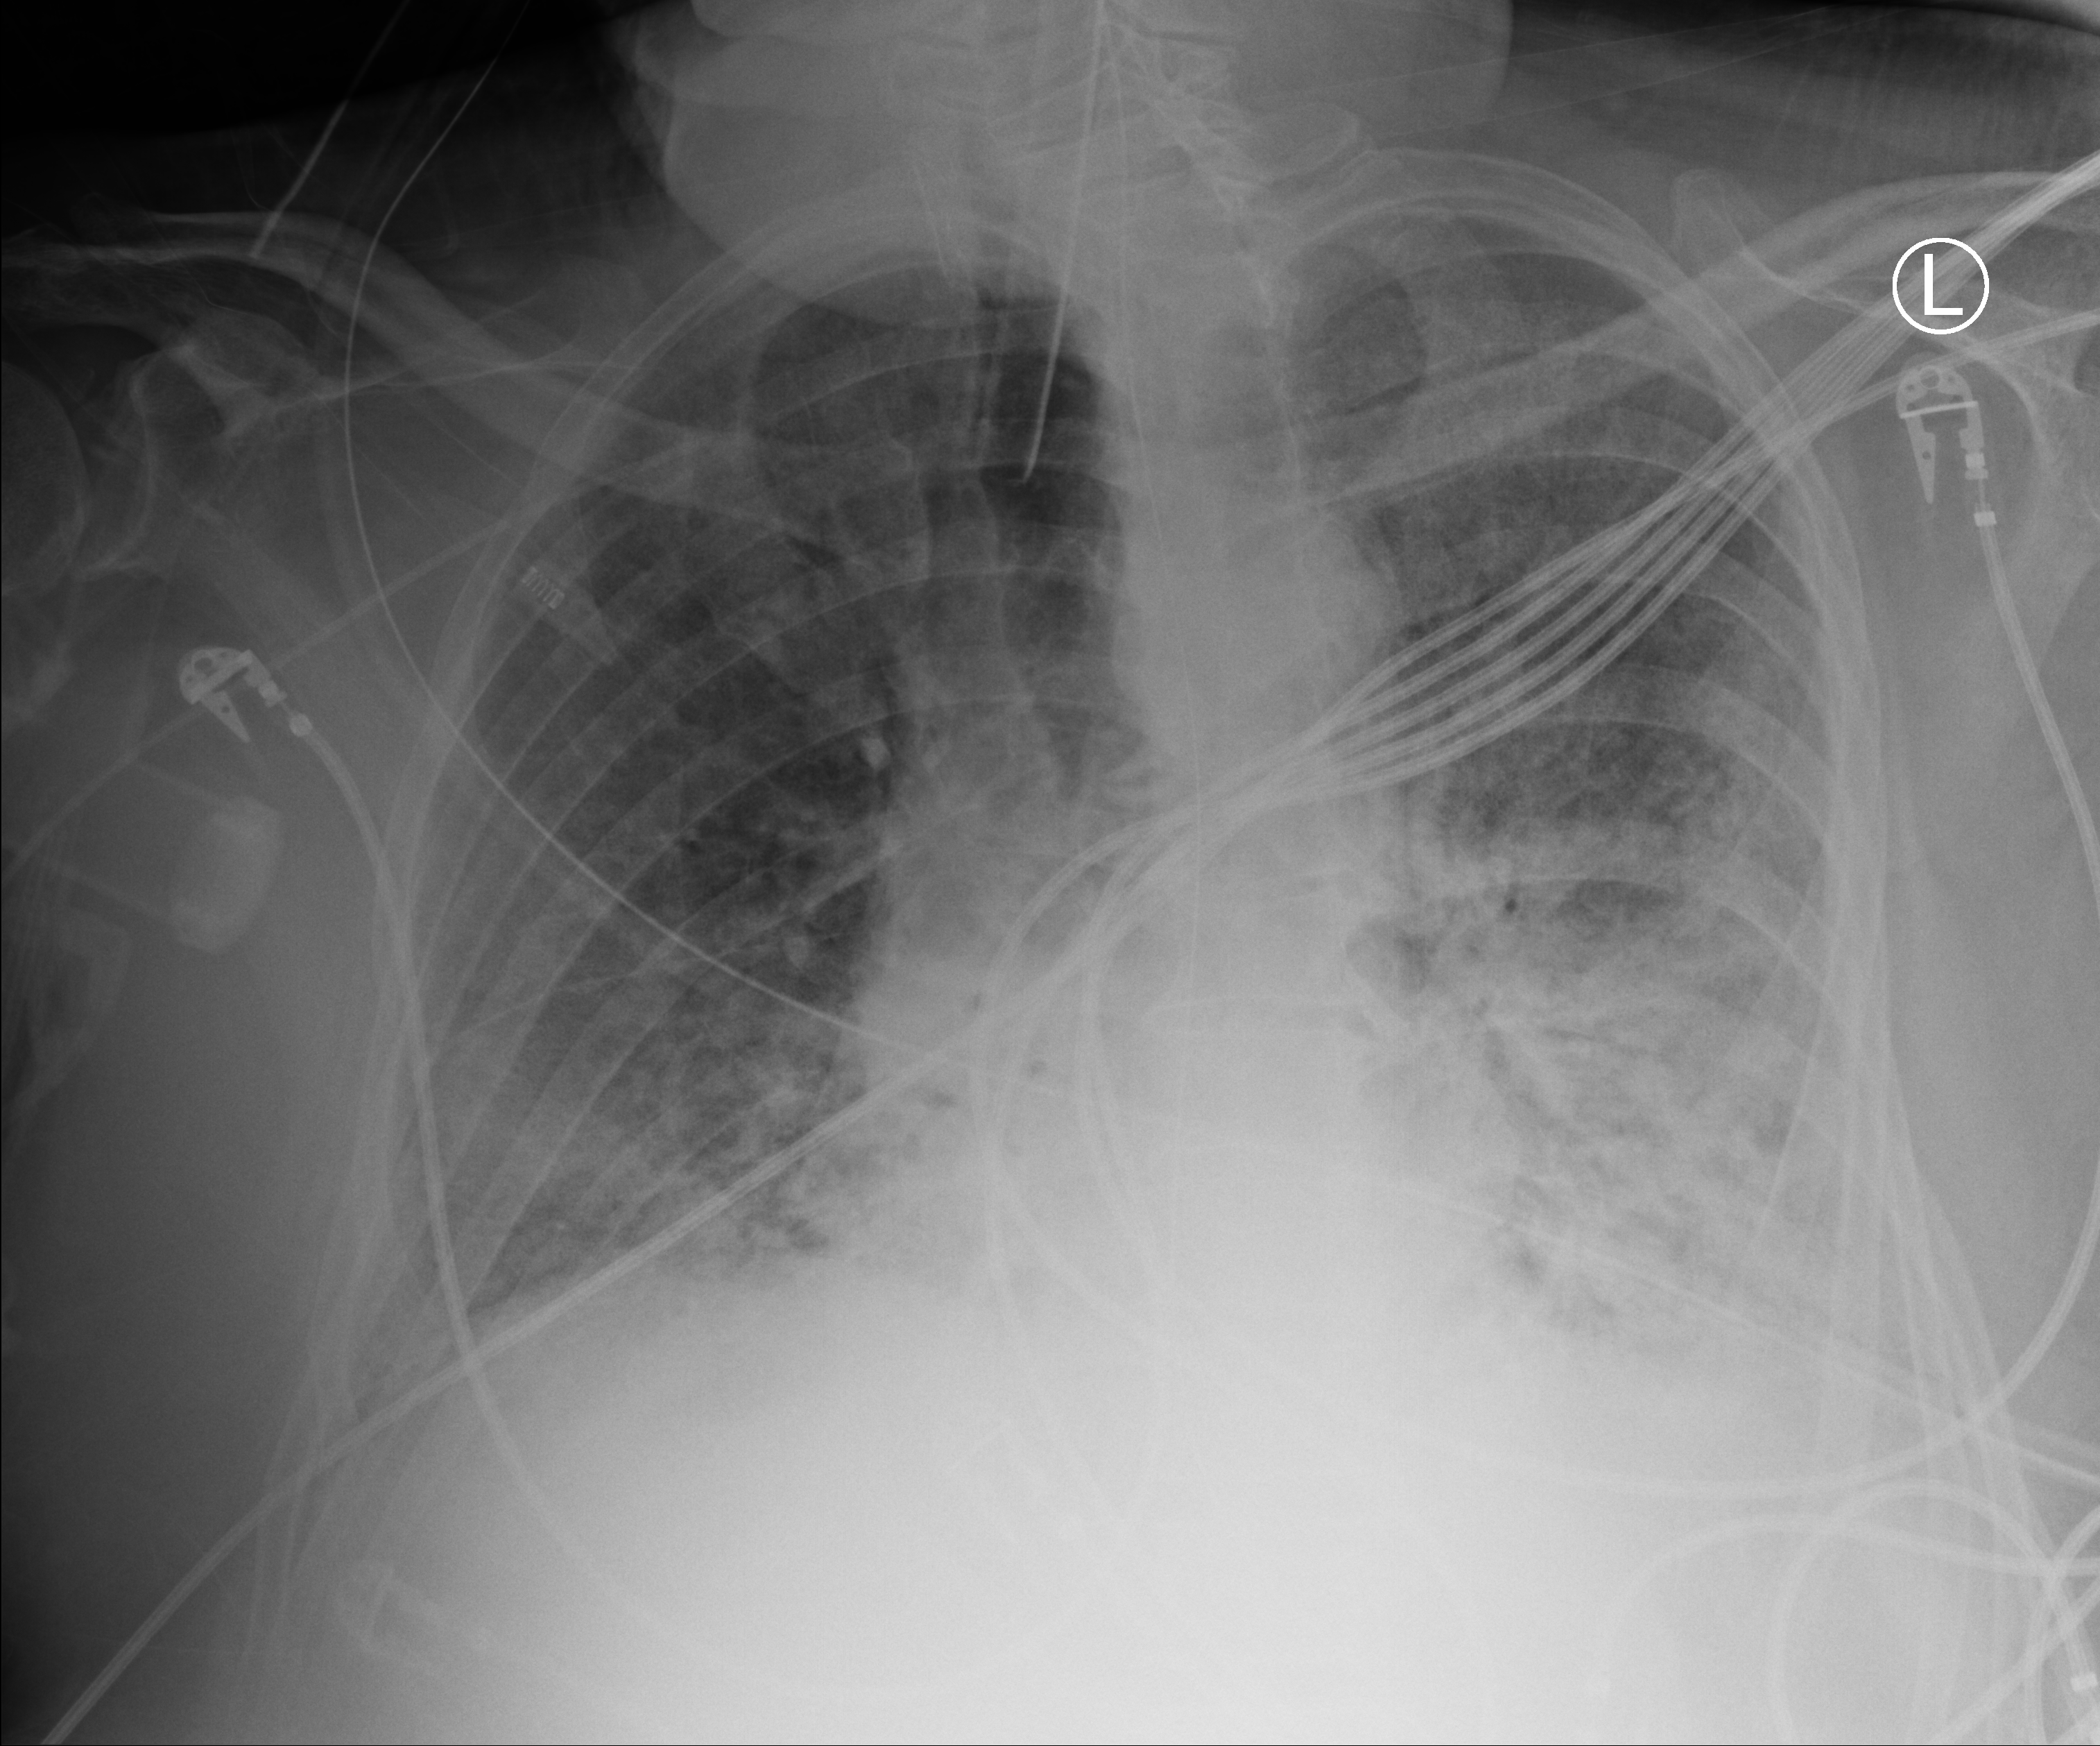
Bedside chest radiograph (computed radiography), anteroposterior (AP) projection. Patient hospitalised with COVID-19; male, aged 60–74 years.
From the hospital-stay record, not from the radiograph (when in the stay this image was taken is not recorded):
- mechanically ventilated during this hospital stay: yes
- admitted to intensive care during this hospital stay: yes
- smoking status (admission record): former